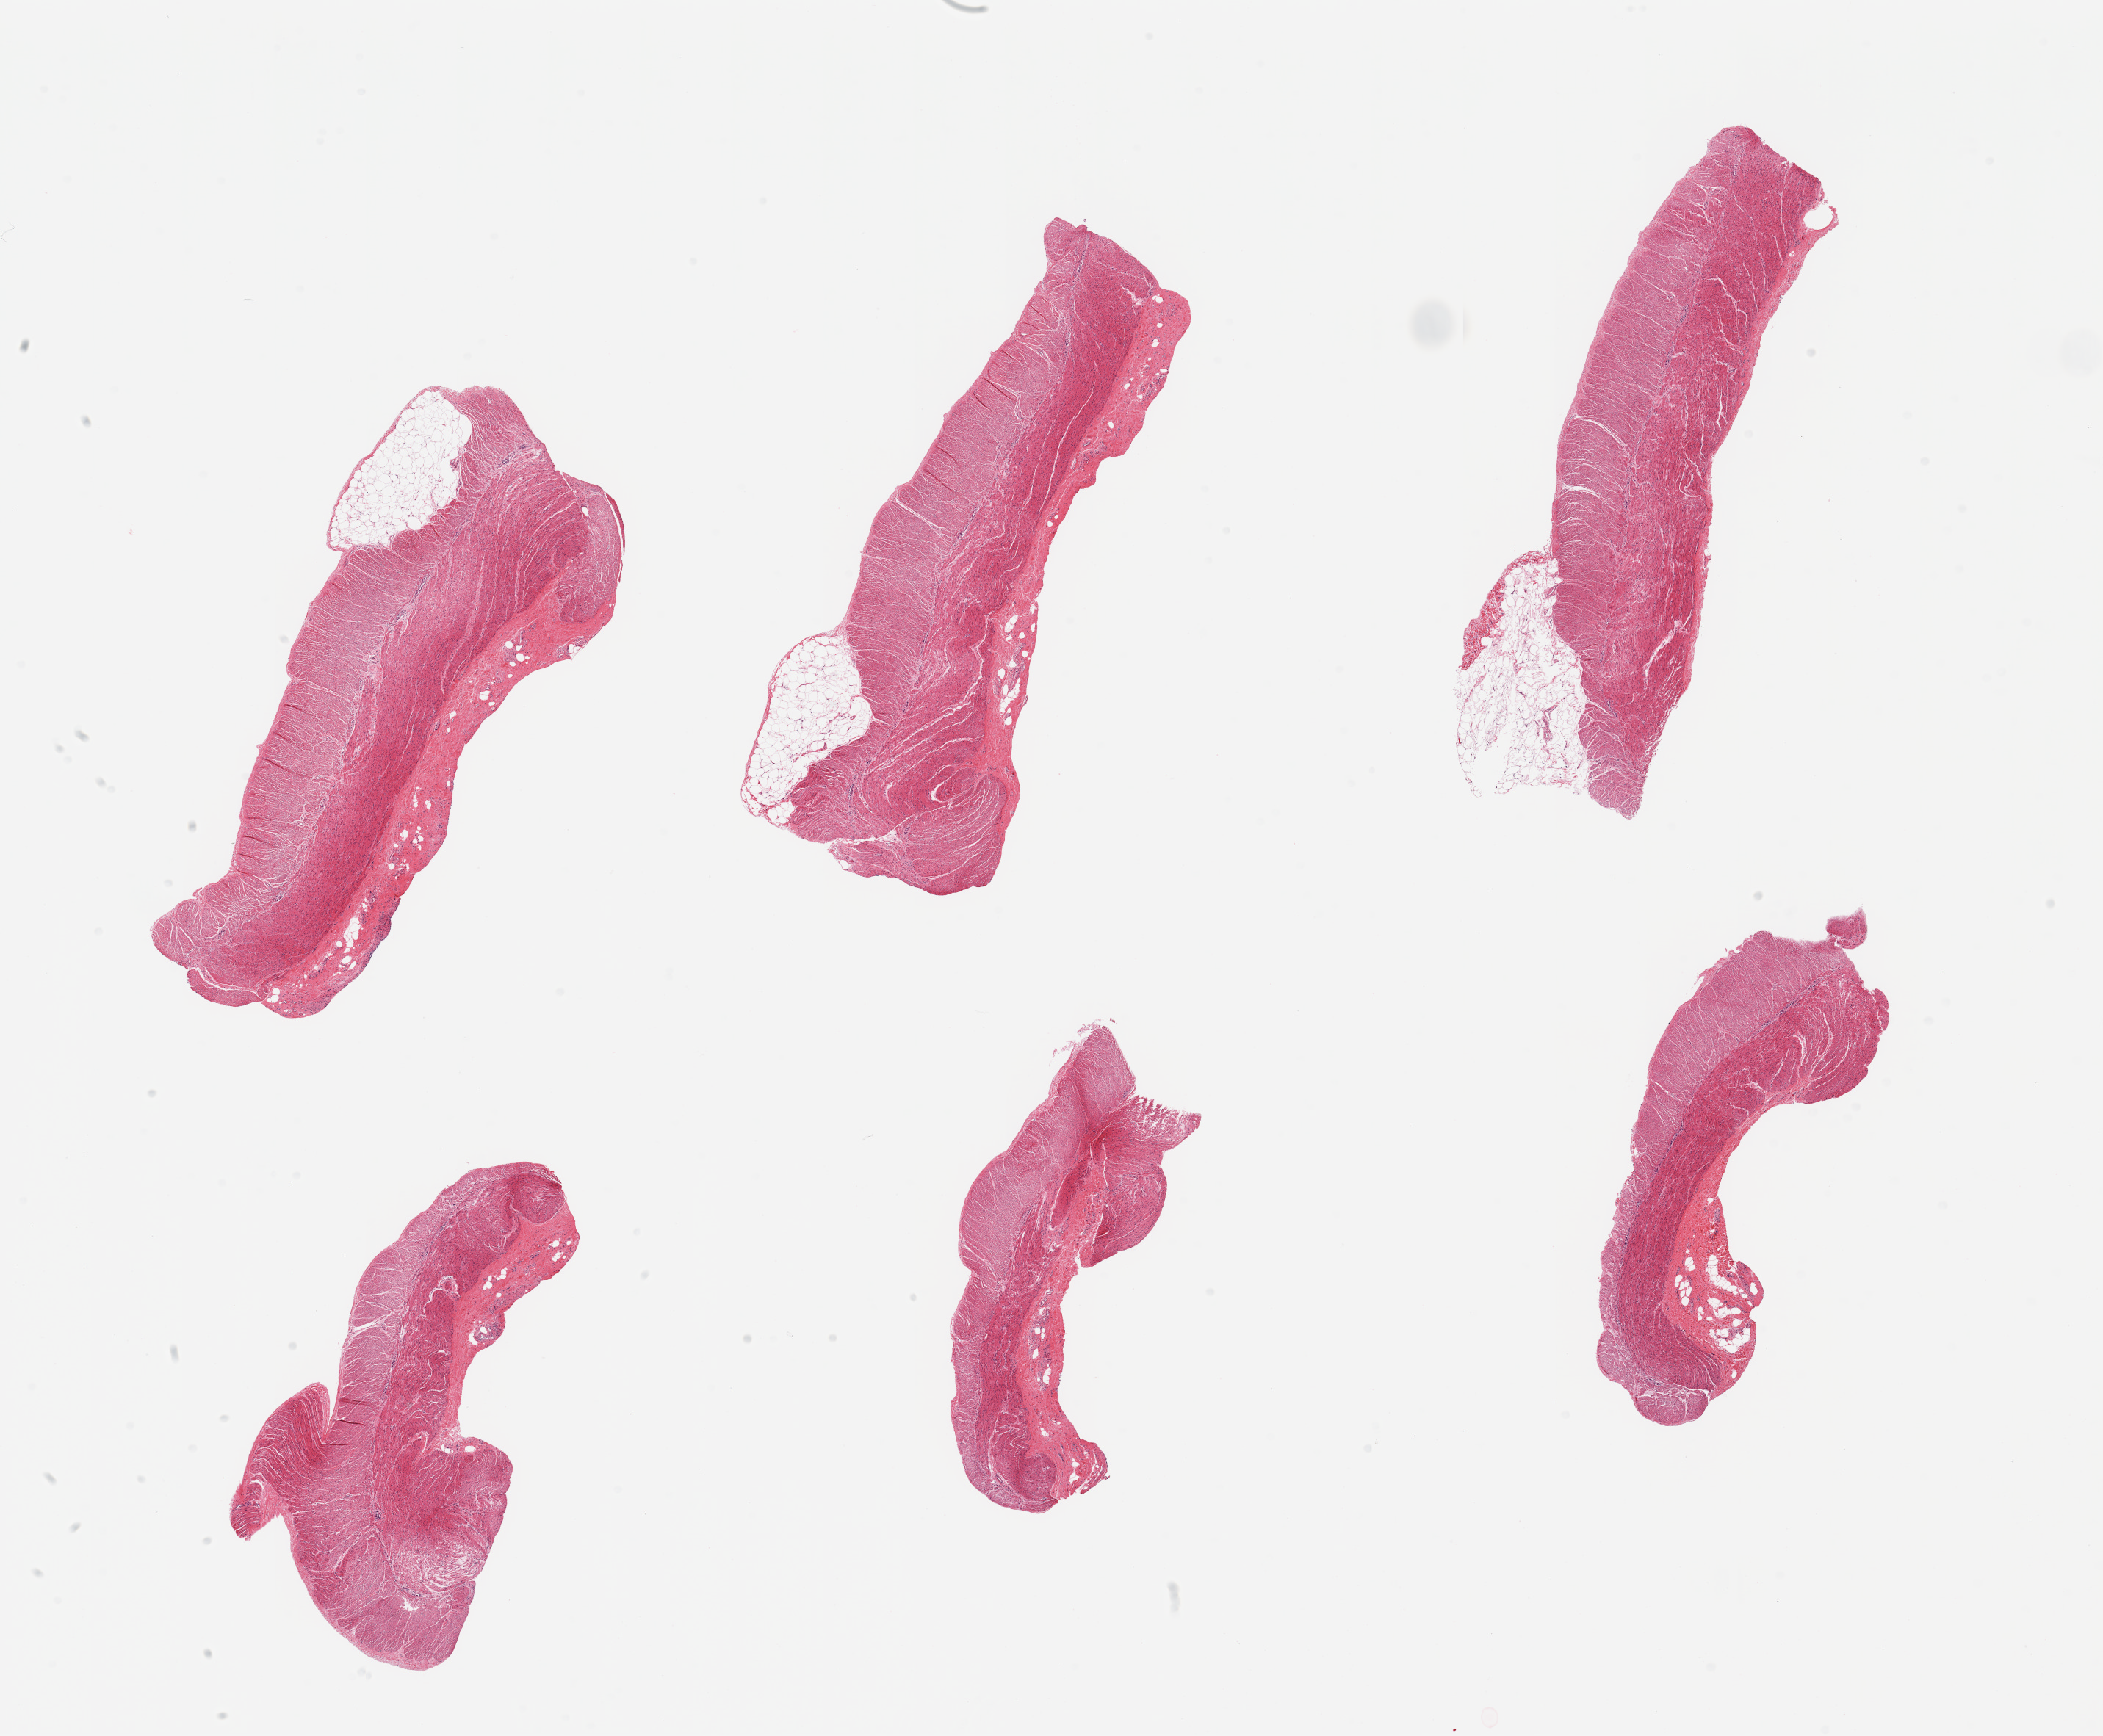
Whole-slide image, H&E stain, a low-resolution overview of the entire scanned area, about 22.6 x 18.7 mm; PAXgene-fixed, paraffin-embedded tissue; sampled site (target tissue): sigmoid colon; tissue donor sample. Male donor.
Review note (as recorded): 6 pieces; target muscularis with small attachment of fat on 3 pieces.